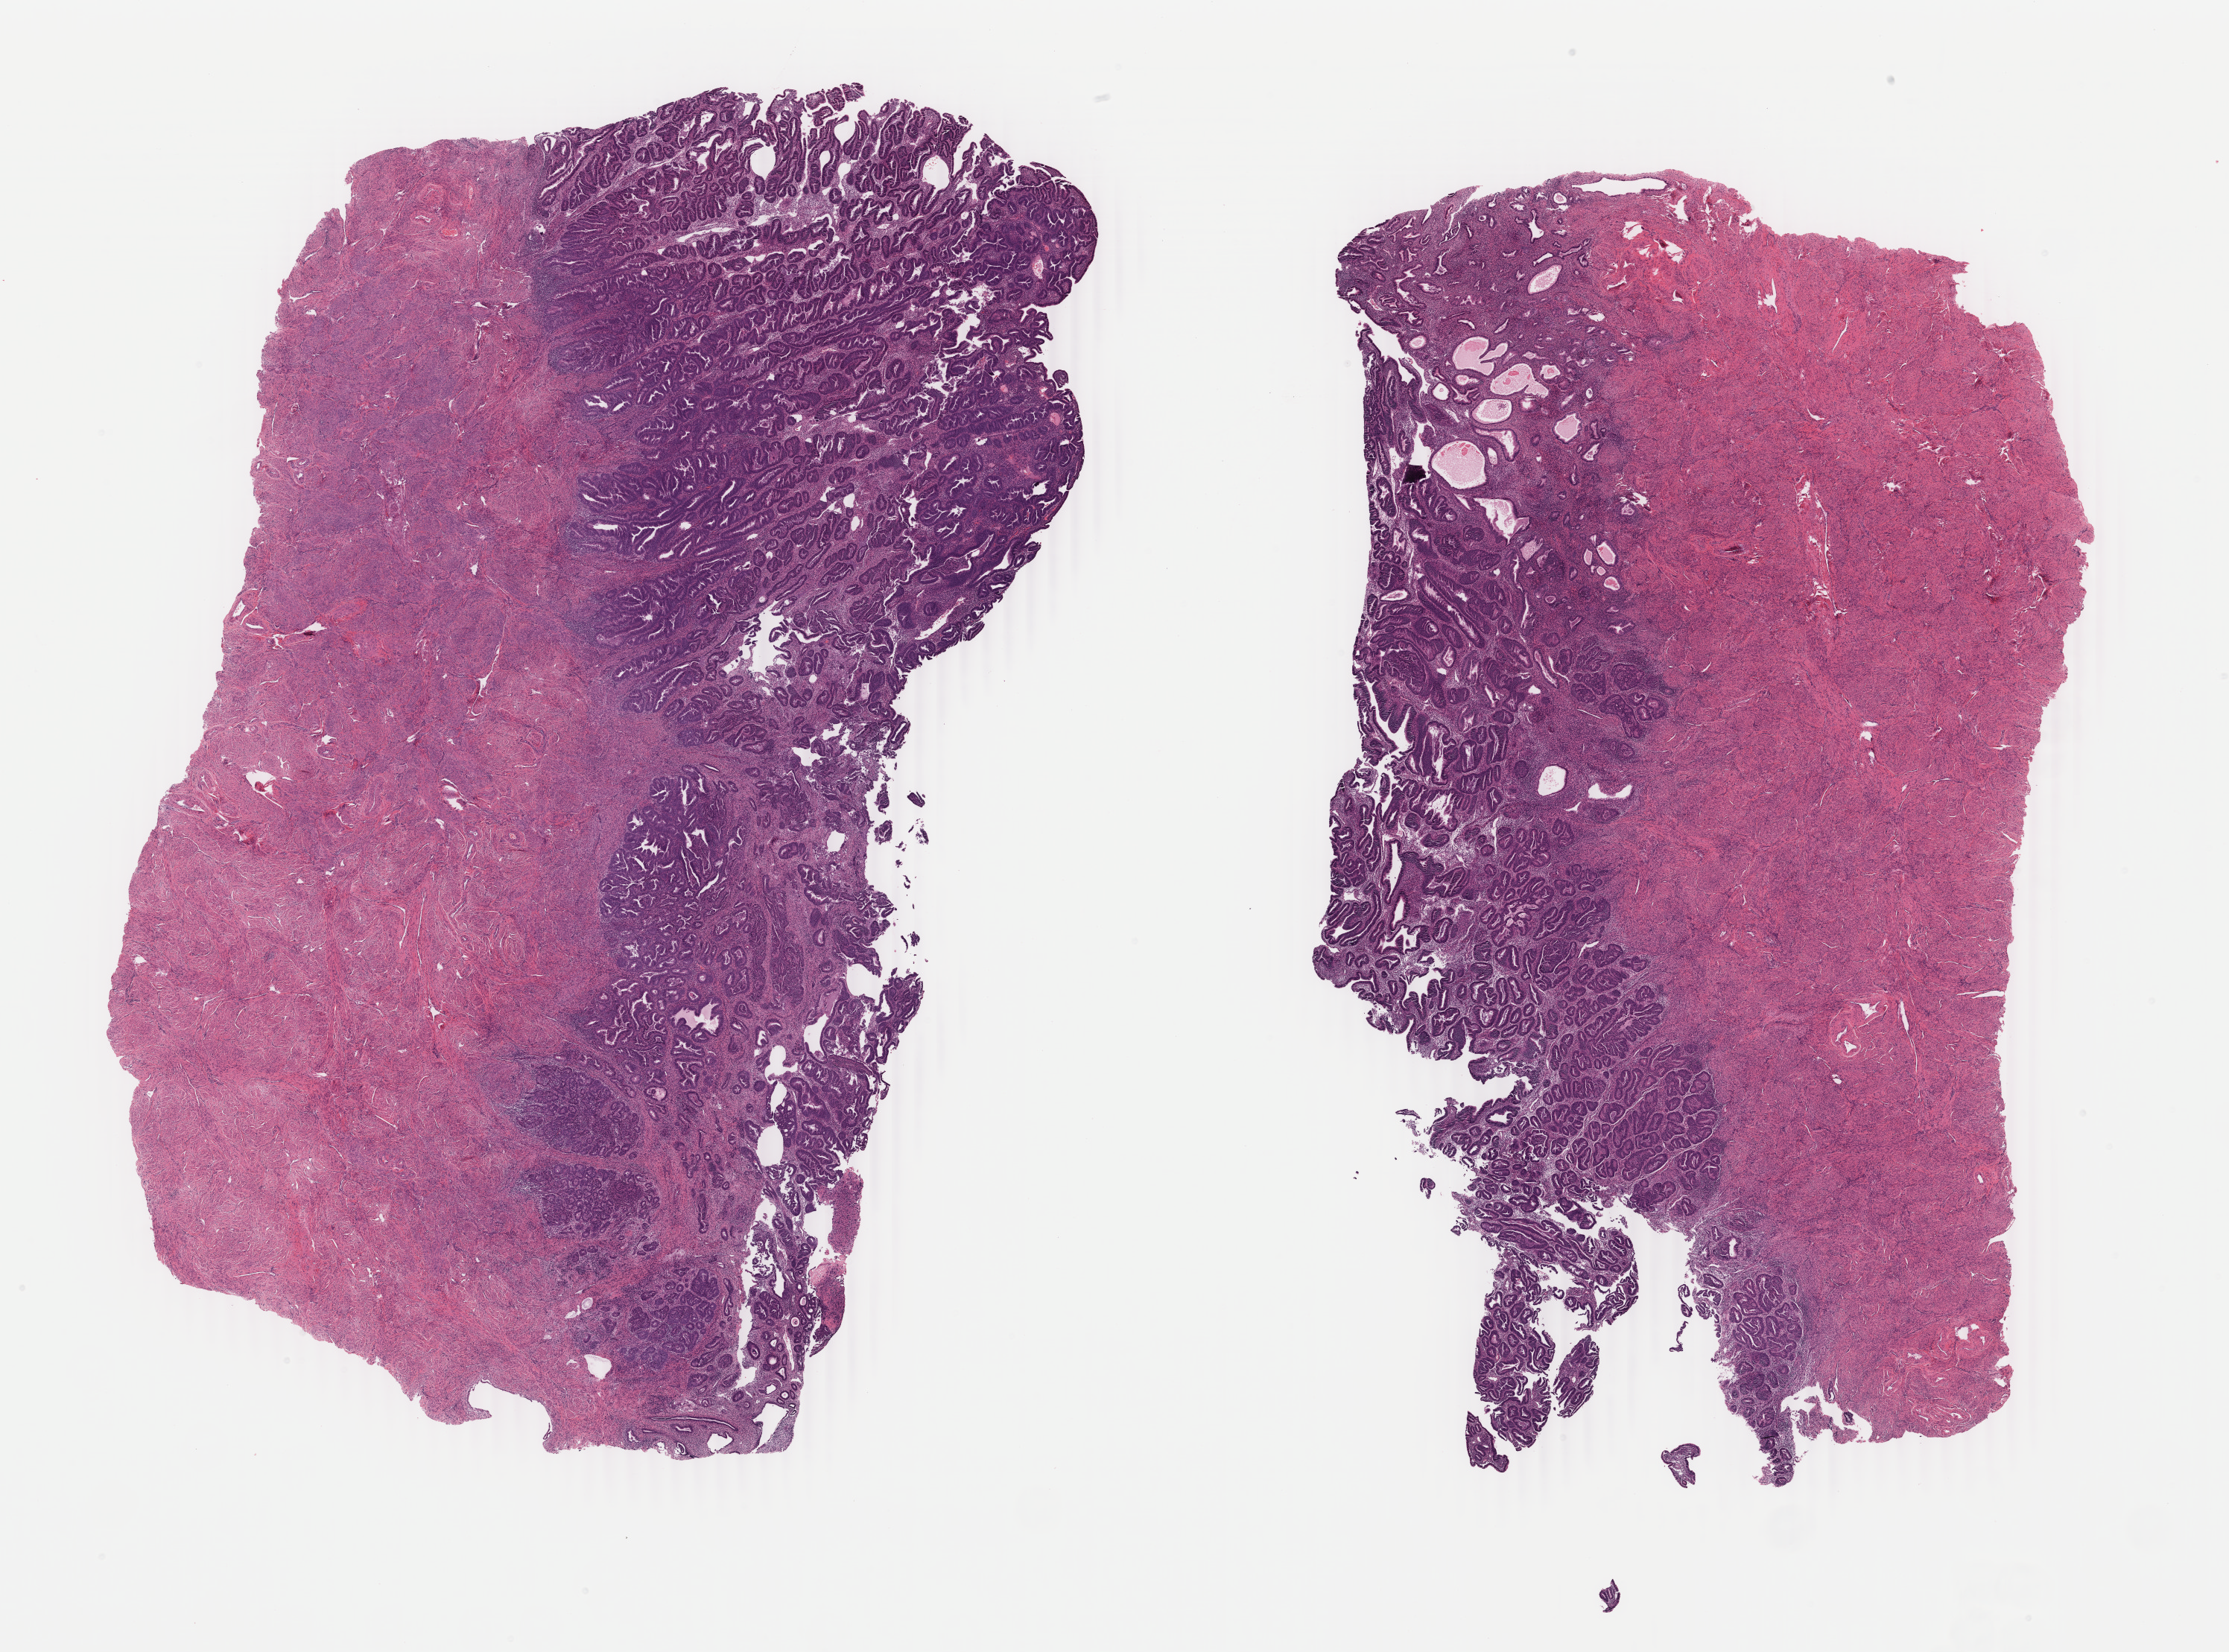
Digitized Hematoxylin and eosin (H&E) stained tissue section (whole slide), whole scanned area (about 23.8 x 17.6 mm, acquisition: 40x scan) shown as a low-resolution overview. Formalin-fixed paraffin-embedded (FFPE) diagnostic section. Uterus, primary tumour sample. Patient: female, age at initial diagnosis 48 years. Histologic grade: G3 (poorly differentiated).
FIGO stage: IC. Lymph nodes positive (case pathology): 0 of 17 examined. Diagnosis: Endometrioid adenocarcinoma, NOS (endometrium).